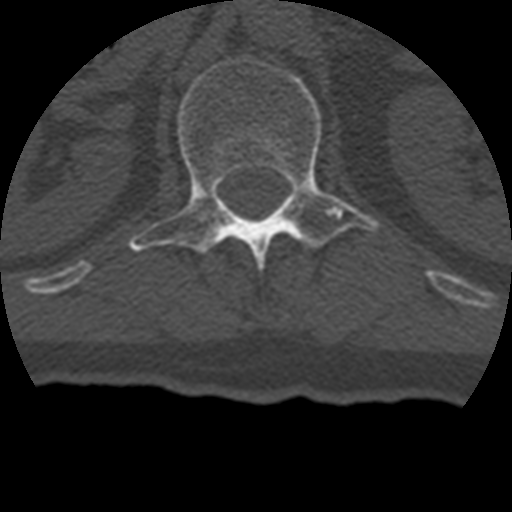
CT including the spine, one axial slice; slice 146 of 399 in the series (ordered by position); reconstruction kernel STANDARD; bone window (W 1800 / L 400 HU); 512 × 512 image matrix, field of view 160 × 160 mm. Patient age 69 years. Case-level facts recorded for this patient, not image findings: primary cancer: prostate.
Annotated regions visible in this slice (semi-automatically segmented with operator editing):
- L1 vertebra: bounding box <128,54,379,267> (left, top, right, bottom; pixels)